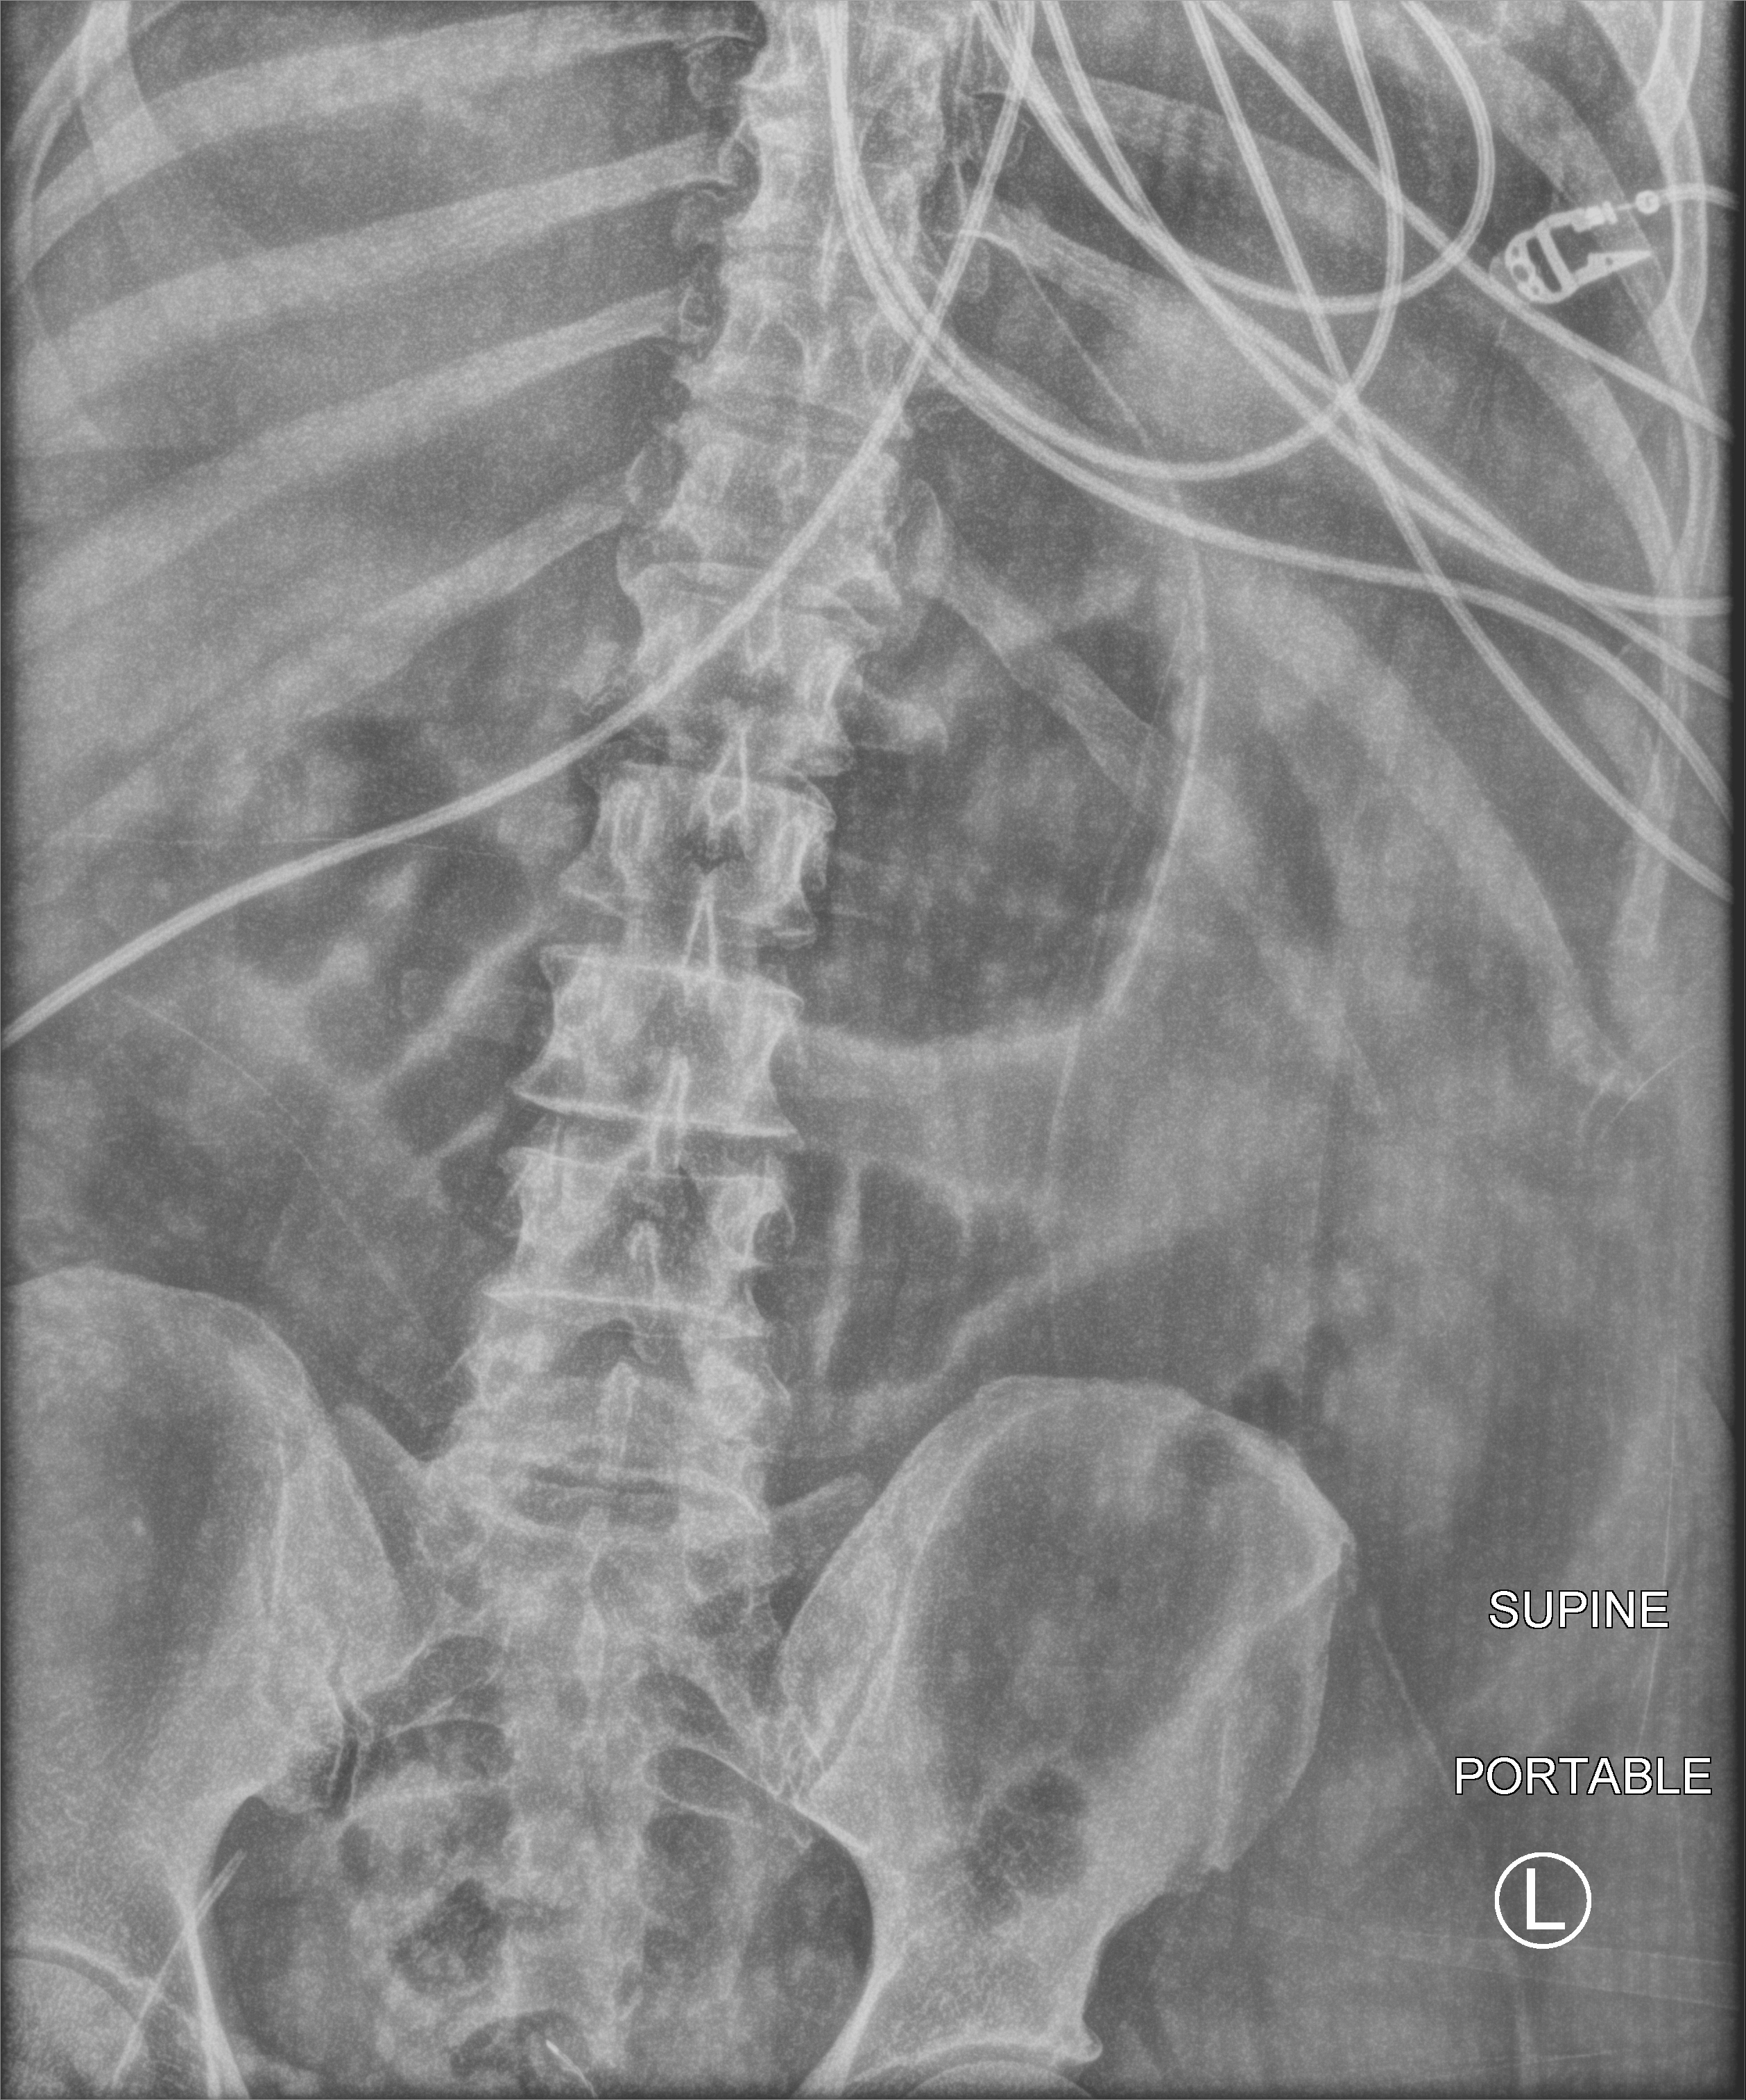
Abdomen X-ray (portable); anteroposterior (AP) projection. Male patient hospitalised with COVID-19, age 60–74 years.
Hospital-stay facts (about this admission, not read from this image; timing relative to this image not recorded):
- mechanically ventilated during this hospital stay: yes
- other chronic lung disease (admission record): no
- admitted to intensive care during this hospital stay: yes